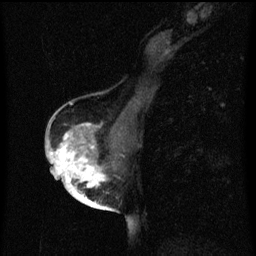
Breast MRI (dynamic contrast-enhanced), one sagittal slice. Position 32 of 60 along the scan axis. Dynamic contrast-enhanced series, image 2 of 3 at this slice position (ordered by acquisition). 1.5 T. TE 4.2 ms, TR 8 ms. 2 mm slice thickness. 256 × 256 image matrix, field of view 180 × 180 mm. Female patient, age 56 years.
Structures marked on this image (semi-automatic segmentation, software-assisted and operator-edited):
- analysis volume of interest (the breast-tissue region the enhancement analysis was run in; not a lesion): bounding box (x1, y1, x2, y2) in pixels: (54, 124, 120, 199)
- tumour enhancement mask (voxels above the 70 % enhancement threshold inside the analysis volume of interest): (54, 124, 107, 199)